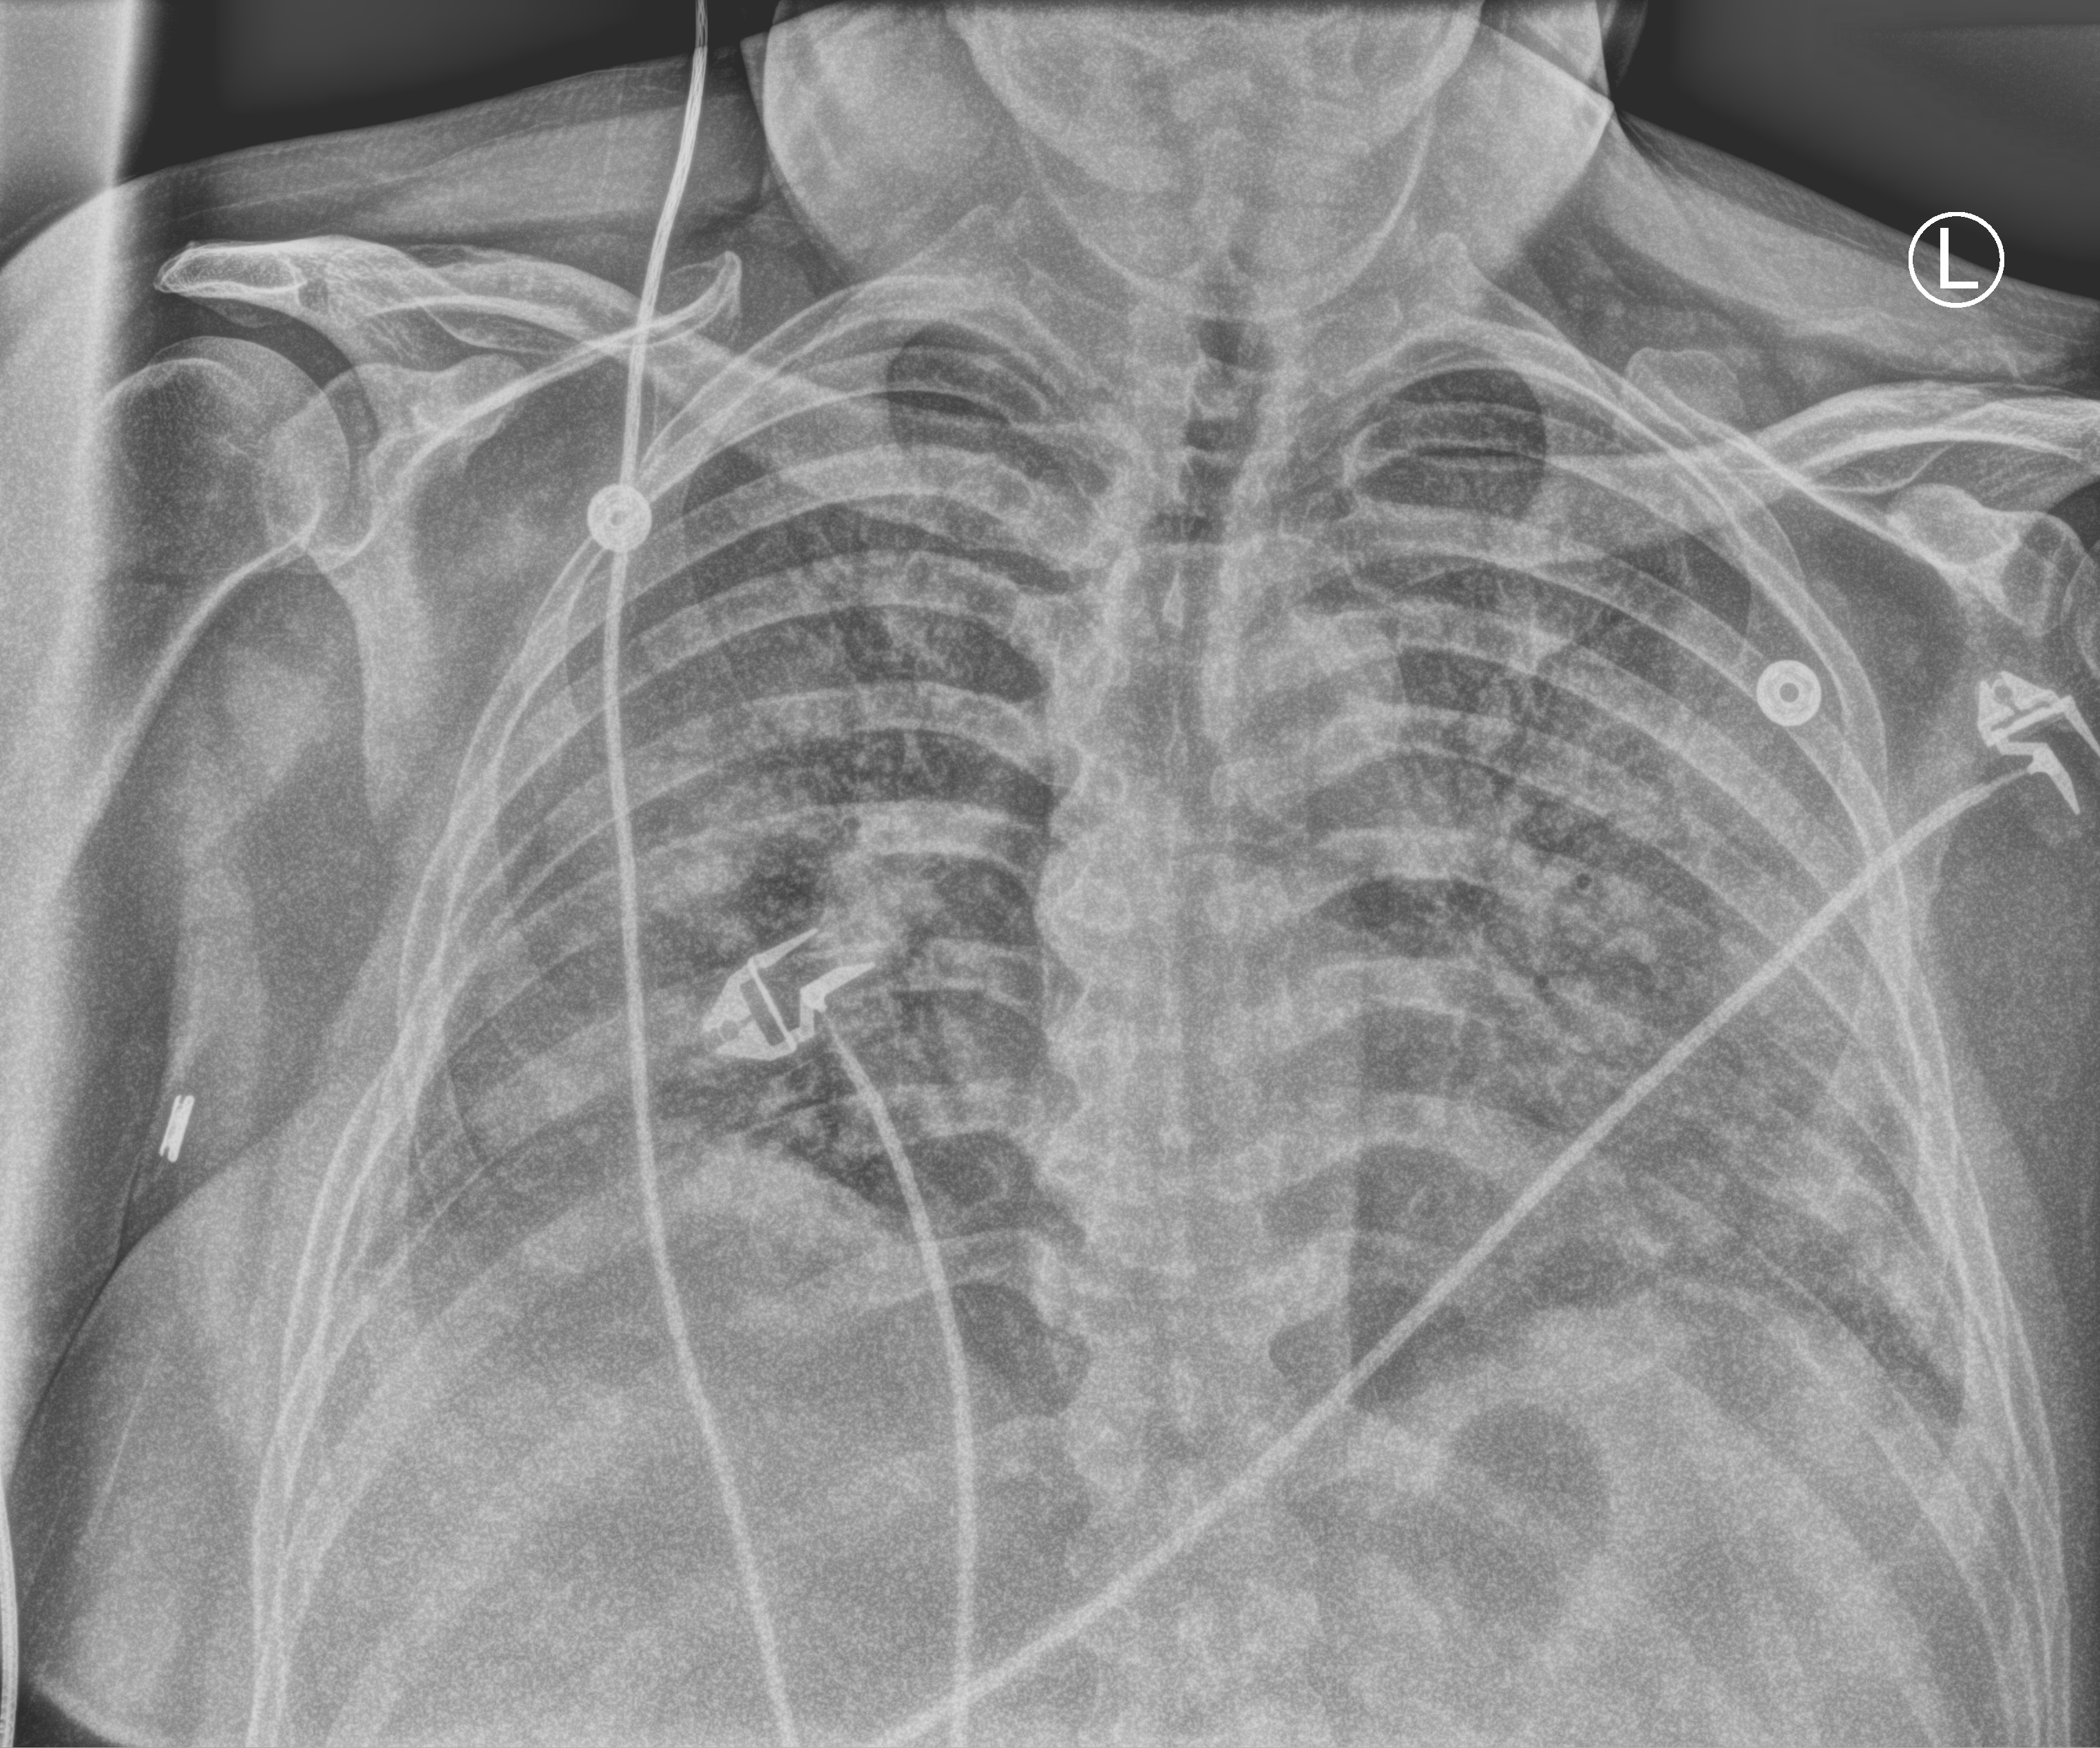
Portable chest radiograph; anteroposterior (AP) projection. Male patient hospitalised with COVID-19, age 18–59 years.
Admission-level facts for this patient (not findings on this image; timing relative to this image not recorded): admitted to intensive care during this hospital stay: yes; length of hospital stay: 24 days; mechanically ventilated during this hospital stay: yes.